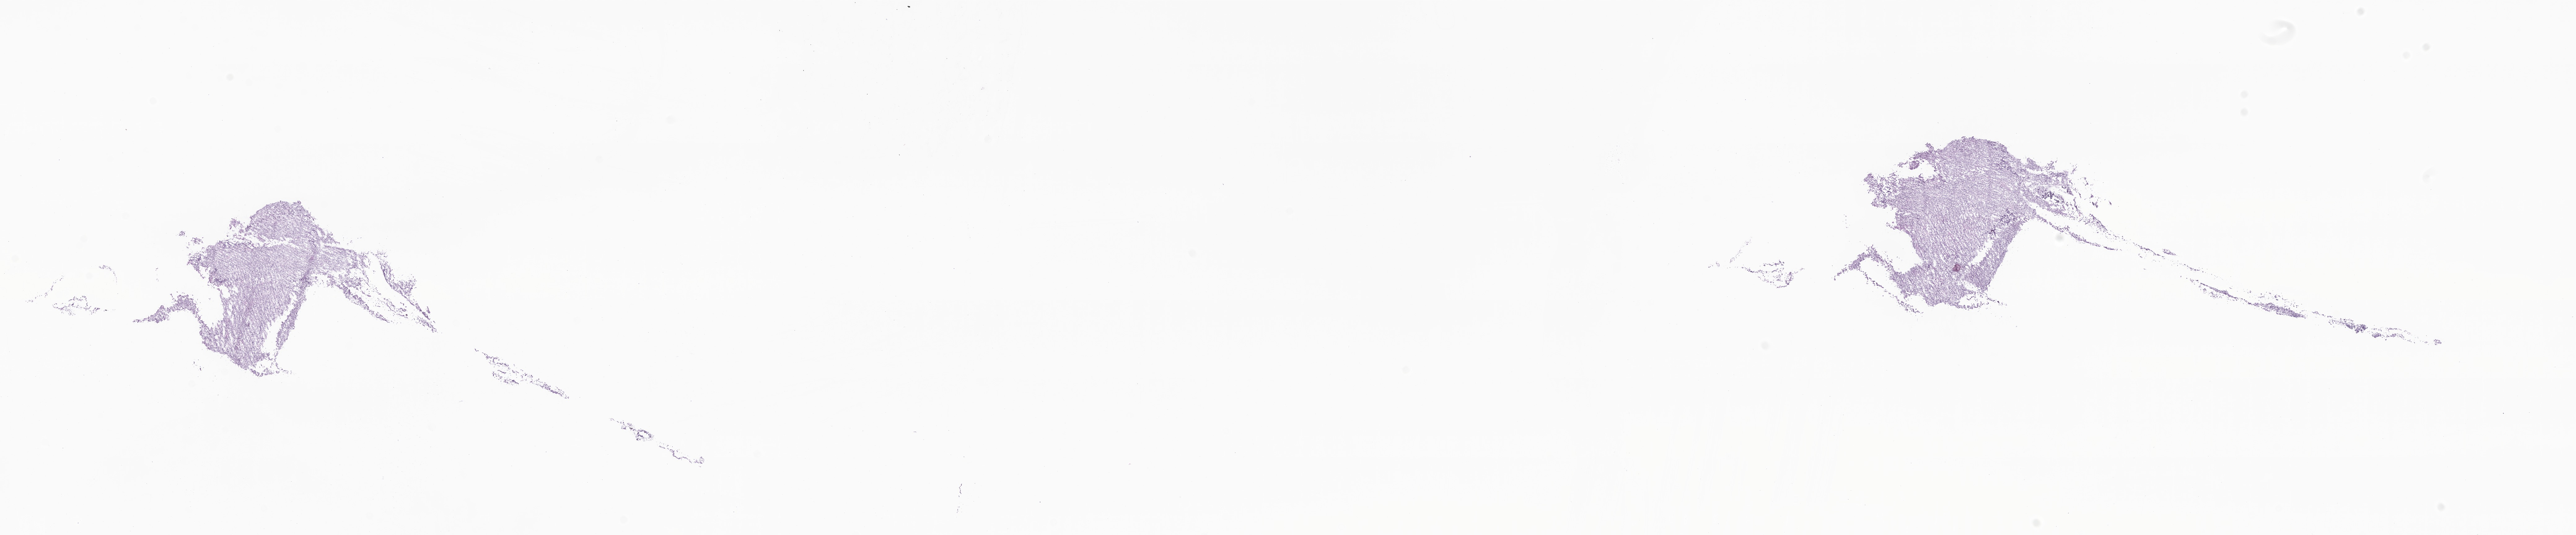
Haematoxylin and eosin whole-slide image of tumor tissue from the cerebellum, whole scanned area (about 35.1 x 7.3 mm) shown as a low-resolution overview; cryosection (OCT / tissue freezing medium). Patient: male, age 136 months (11 years 4 months).
Recorded diagnosis: Medulloblastoma, NOS.